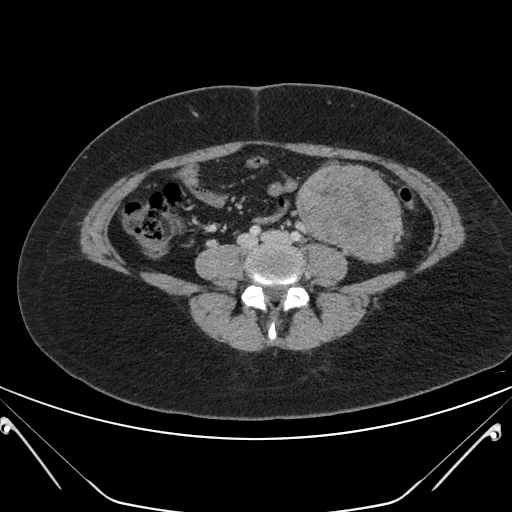
Contrast-enhanced abdominal CT, one axial slice. Slice 73 of 168 in the series (ordered by position). 120 kVp. Intravenous contrast given. Soft-tissue window (W 400 / L 40 HU). 512 × 512 image matrix, field of view 394 × 394 mm. Female patient, age 26 years. From the clinical record (not read from this slice): diagnosis: adrenocortical carcinoma; tumour side: left adrenal; tumour size at pathology: 28 cm; Ki-67 index: 20 %; stage (as recorded): 2.
Annotated regions visible in this slice (semi-automatic segmentation, software-assisted and operator-edited):
- mass: bounding box (x1, y1, x2, y2) in pixels: (296, 163, 402, 260)